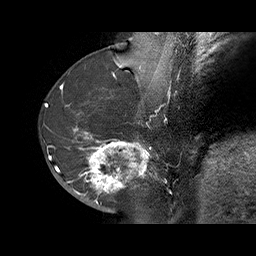
Breast MRI (dynamic contrast-enhanced), one sagittal slice; position 26 of 70 along the scan axis; dynamic contrast-enhanced series, time point 2 of 6 at this slice position (early post-contrast); 1.5 T; TE 4.5 ms, TR 32.4 ms; 3 mm slice thickness; 256 × 256 image matrix, field of view 180 × 180 mm. Female patient. Case-level facts recorded for this patient, not image findings: setting: breast cancer imaged before/during neoadjuvant chemotherapy; receptor status: HR-positive, HER2-negative.
Structures marked on this image (semi-automatic segmentation, software-assisted and operator-edited):
- analysis volume of interest (the breast-tissue region the enhancement analysis was run in; not a lesion): bounding box <71,128,159,202> (left, top, right, bottom; pixels)
- tumour enhancement mask (voxels above the 100 % enhancement threshold inside the analysis volume of interest): <73,128,150,201>